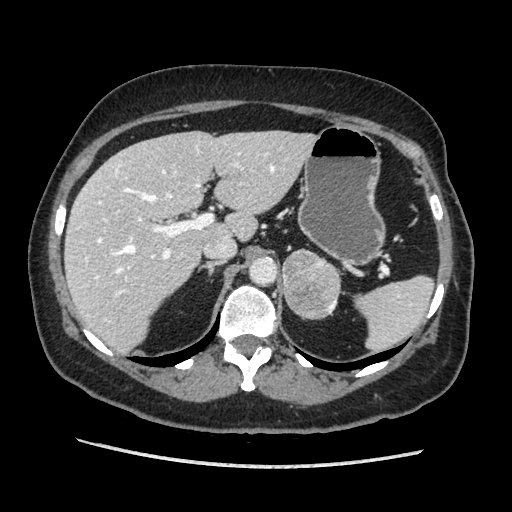
Contrast-enhanced abdominal CT, one axial slice; position 131 of 203 along the scan axis; soft-tissue window (W 400 / L 40 HU); 1.25 mm slice thickness; 512 × 512 image matrix, field of view 360 × 360 mm. Female patient. Case-level facts recorded for this patient, not image findings: diagnosis: adrenocortical carcinoma; tumour side: left adrenal; tumour size at pathology: 6.5 cm; Ki-67 index: 22 %; stage (as recorded): 2.
Annotated regions visible in this slice (semi-automatic segmentation, software-assisted and operator-edited):
- mass: bounding box (x1, y1, x2, y2) in pixels: (282, 249, 340, 318)